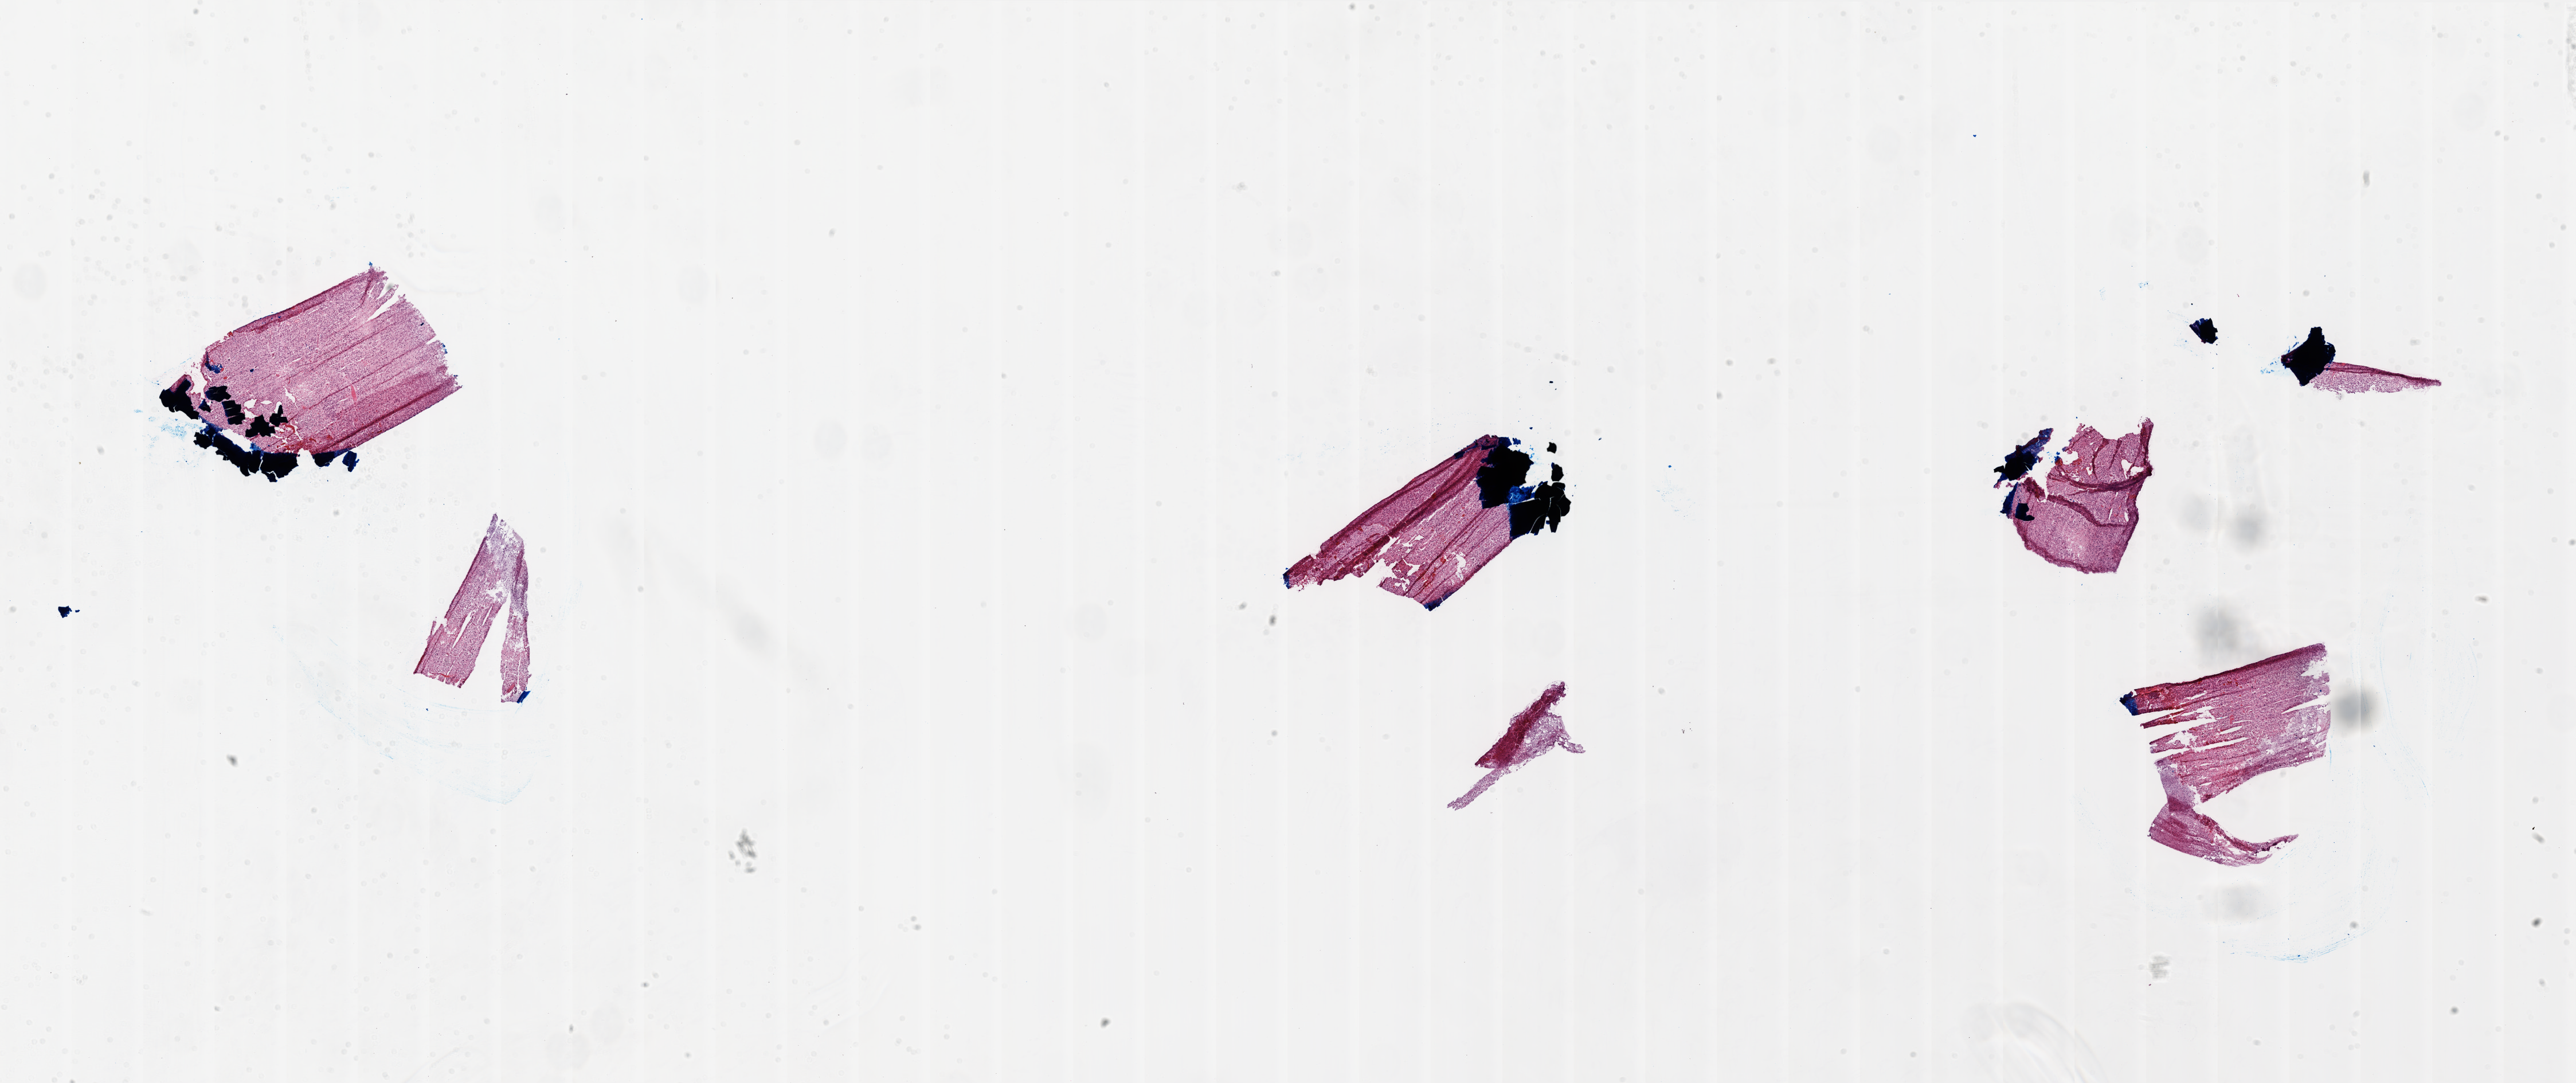
Whole-slide histology image, Hematoxylin and eosin (H&E) stained, shown as a low-resolution overview of the whole scanned area (about 36.0 x 15.1 mm, slide scanned at 20x). Frozen section from the top of the tissue portion. Brain, primary tumour sample. Male patient; age at initial diagnosis 76 years. Composition of this section per pathologist review: tumour cells 90%, tumour nuclei 100%, normal cells 0%, stromal cells 0%, necrosis 10%.
• diagnosis: Glioblastoma